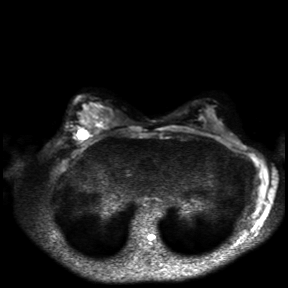
Breast MRI, one axial slice. Slice 19 of 30 in the series (ordered by position). Diffusion-weighted series; image 2 of 4 stored at this slice position (different b-values; order by instance number). 3 T. 4 mm slice thickness. 288 × 288 image matrix, field of view 360 × 360 mm. Female patient.
Structures marked on this image (expert manual segmentation):
- tumour on diffusion-weighted imaging: bounding box <76,130,89,139> (left, top, right, bottom; pixels)